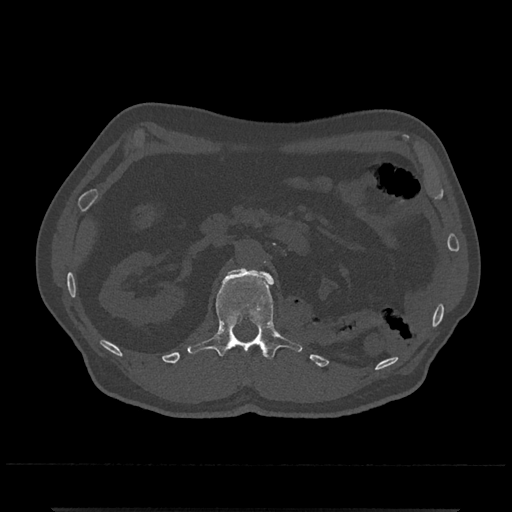
CT including the spine, one axial slice; slice 364 of 797 in the series (ordered by position); 120 kVp; bone window (W 1800 / L 400 HU); 512 × 512 image matrix. Patient: male, 67 years. Case-level facts recorded for this patient, not image findings: primary cancer: prostate.
Structures marked on this image (semi-automatically segmented with operator editing):
- L1 vertebra: bounding box <187,268,303,359> (left, top, right, bottom; pixels)